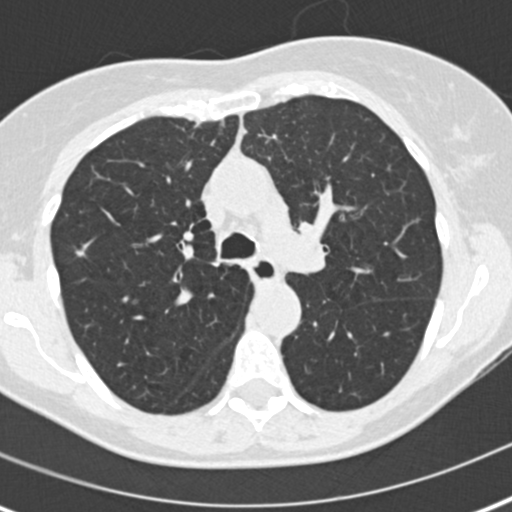
Chest CT (low-dose screening protocol), one axial image; second screening round (one year after baseline); lung window (W 1500 / L -600 HU); 2 mm slice thickness; standard (soft-tissue) reconstruction kernel (B30f); slice 66 of 186 in the series; 512 × 512 image matrix. Female, age 60 years at enrolment. Current smoker at enrolment.
• Lesion marked by an expert reader, box from (x=55, y=230) to (x=101, y=274) px.
• Reader record for this screening exam (exam-level; its link to the box is not recorded): non-calcified nodule or mass ≥4 mm, right upper lobe, 8 × 6 mm, spiculated (stellate) margins, soft tissue attenuation, pre-existing on the prior screen: no.
• Lung cancer was diagnosed 511 days after this screen: bronchiolo-alveolar adenocarcinoma, NOS, right upper lobe, well differentiated (G1), stage IA (AJCC 6th edition), 11 mm at pathology.